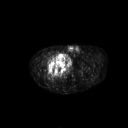
FDG PET of an extremity soft-tissue mass (from a PET/CT study), one axial slice; slice 281 of 311 in the series (ordered by position); 3.27 mm slice thickness; 128 × 128 image matrix, field of view 700 × 700 mm. Patient: male, 50 years. Case-level facts recorded for this patient, not image findings: histological type: undifferentiated - pleiomorphic; grade: high; site of the primary tumour: right thigh.
Annotated regions visible in this slice (expert contour drawn on MRI and transferred to this co-registered scan by the dataset authors):
- gross tumour volume including surrounding oedema: bounding box [x1, y1, x2, y2] px = [50, 52, 65, 68]
- gross tumour volume (mass): [50, 53, 65, 68]